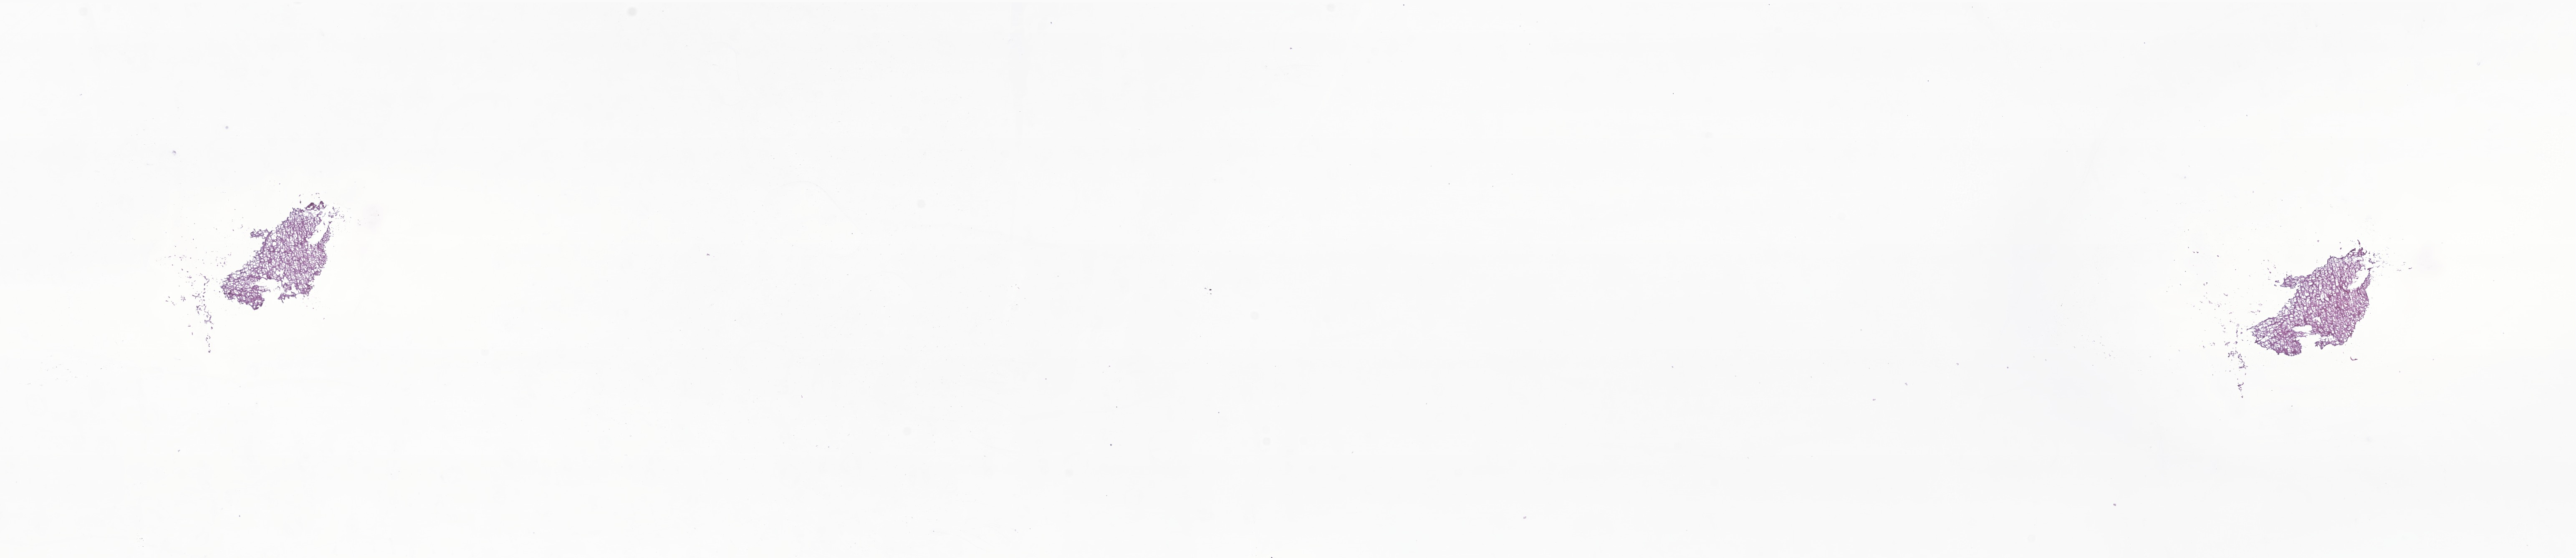
Hematoxylin and eosin (H&E) whole-slide image of tumor tissue from the cerebellum, low-resolution overview of the scanned area, about 26.0 x 5.6 mm. Frozen section (OCT-embedded). Patient: male, age 110 months.
Recorded diagnosis: Pilocytic astrocytoma.